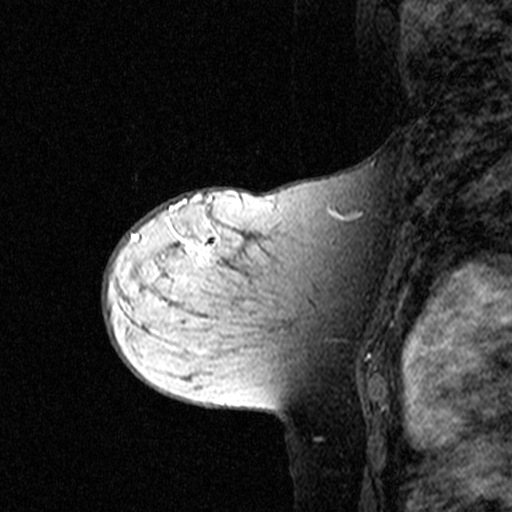
Breast MRI (dynamic contrast-enhanced), one sagittal slice; slice 28 of 44 in the series (ordered by position); dynamic contrast-enhanced study with each time point stored as its own series, time point 2 of 3 at this slice position (early post-contrast, ordered by acquisition time); 1.5 T; TE 4.5 ms, TR 11 ms; 512 × 512 image matrix, field of view 200 × 200 mm. Female patient, age 44 years. From the clinical record (not read from this slice): setting: breast cancer imaged before/during neoadjuvant chemotherapy; receptor status: triple-negative.
Annotated regions visible in this slice (semi-automatic segmentation, software-assisted and operator-edited):
- analysis volume of interest (the breast-tissue region the enhancement analysis was run in; not a lesion): bounding box [x1, y1, x2, y2] px = [142, 208, 349, 363]
- tumour enhancement mask (voxels above the 90 % enhancement threshold inside the analysis volume of interest): [171, 208, 223, 263]